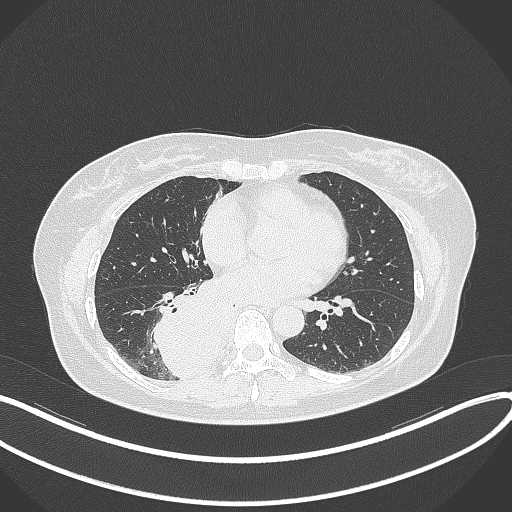
Chest CT, one axial slice; 120 kVp; lung window (W 1500 / L -600 HU); 512 × 512 image matrix. Female patient, age 54 years. Case-level facts recorded for this patient, not image findings: clinical TNM (as recorded): T4 N0 M0.
Structures marked on this image (rectangle marked by the reading radiologist):
- lung tumour (recorded histology: adenocarcinoma): bounding box <151,280,235,382> (left, top, right, bottom; pixels)